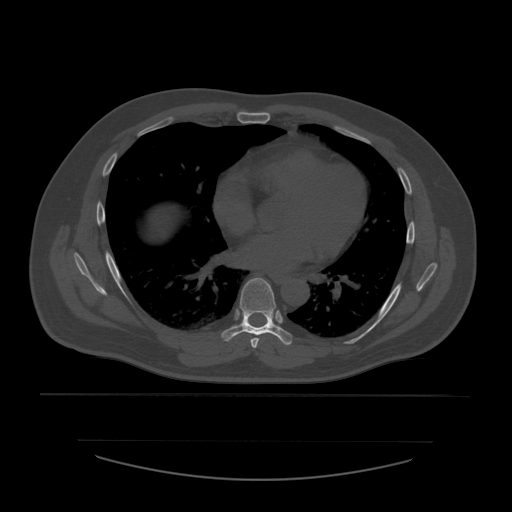
CT including the spine, one axial slice. Reconstruction kernel STANDARD. 120 kVp. Bone window (W 1800 / L 400 HU). 1.25 mm slice thickness. 512 × 512 image matrix, field of view 441 × 441 mm. Patient age 44 years. Case-level facts recorded for this patient, not image findings: primary cancer: soft tissue sarcoma.
Annotated regions visible in this slice (semi-automatically segmented with operator editing):
- T6 vertebra: bounding box <250,338,260,349> (left, top, right, bottom; pixels)
- T7 vertebra: <221,278,293,346>